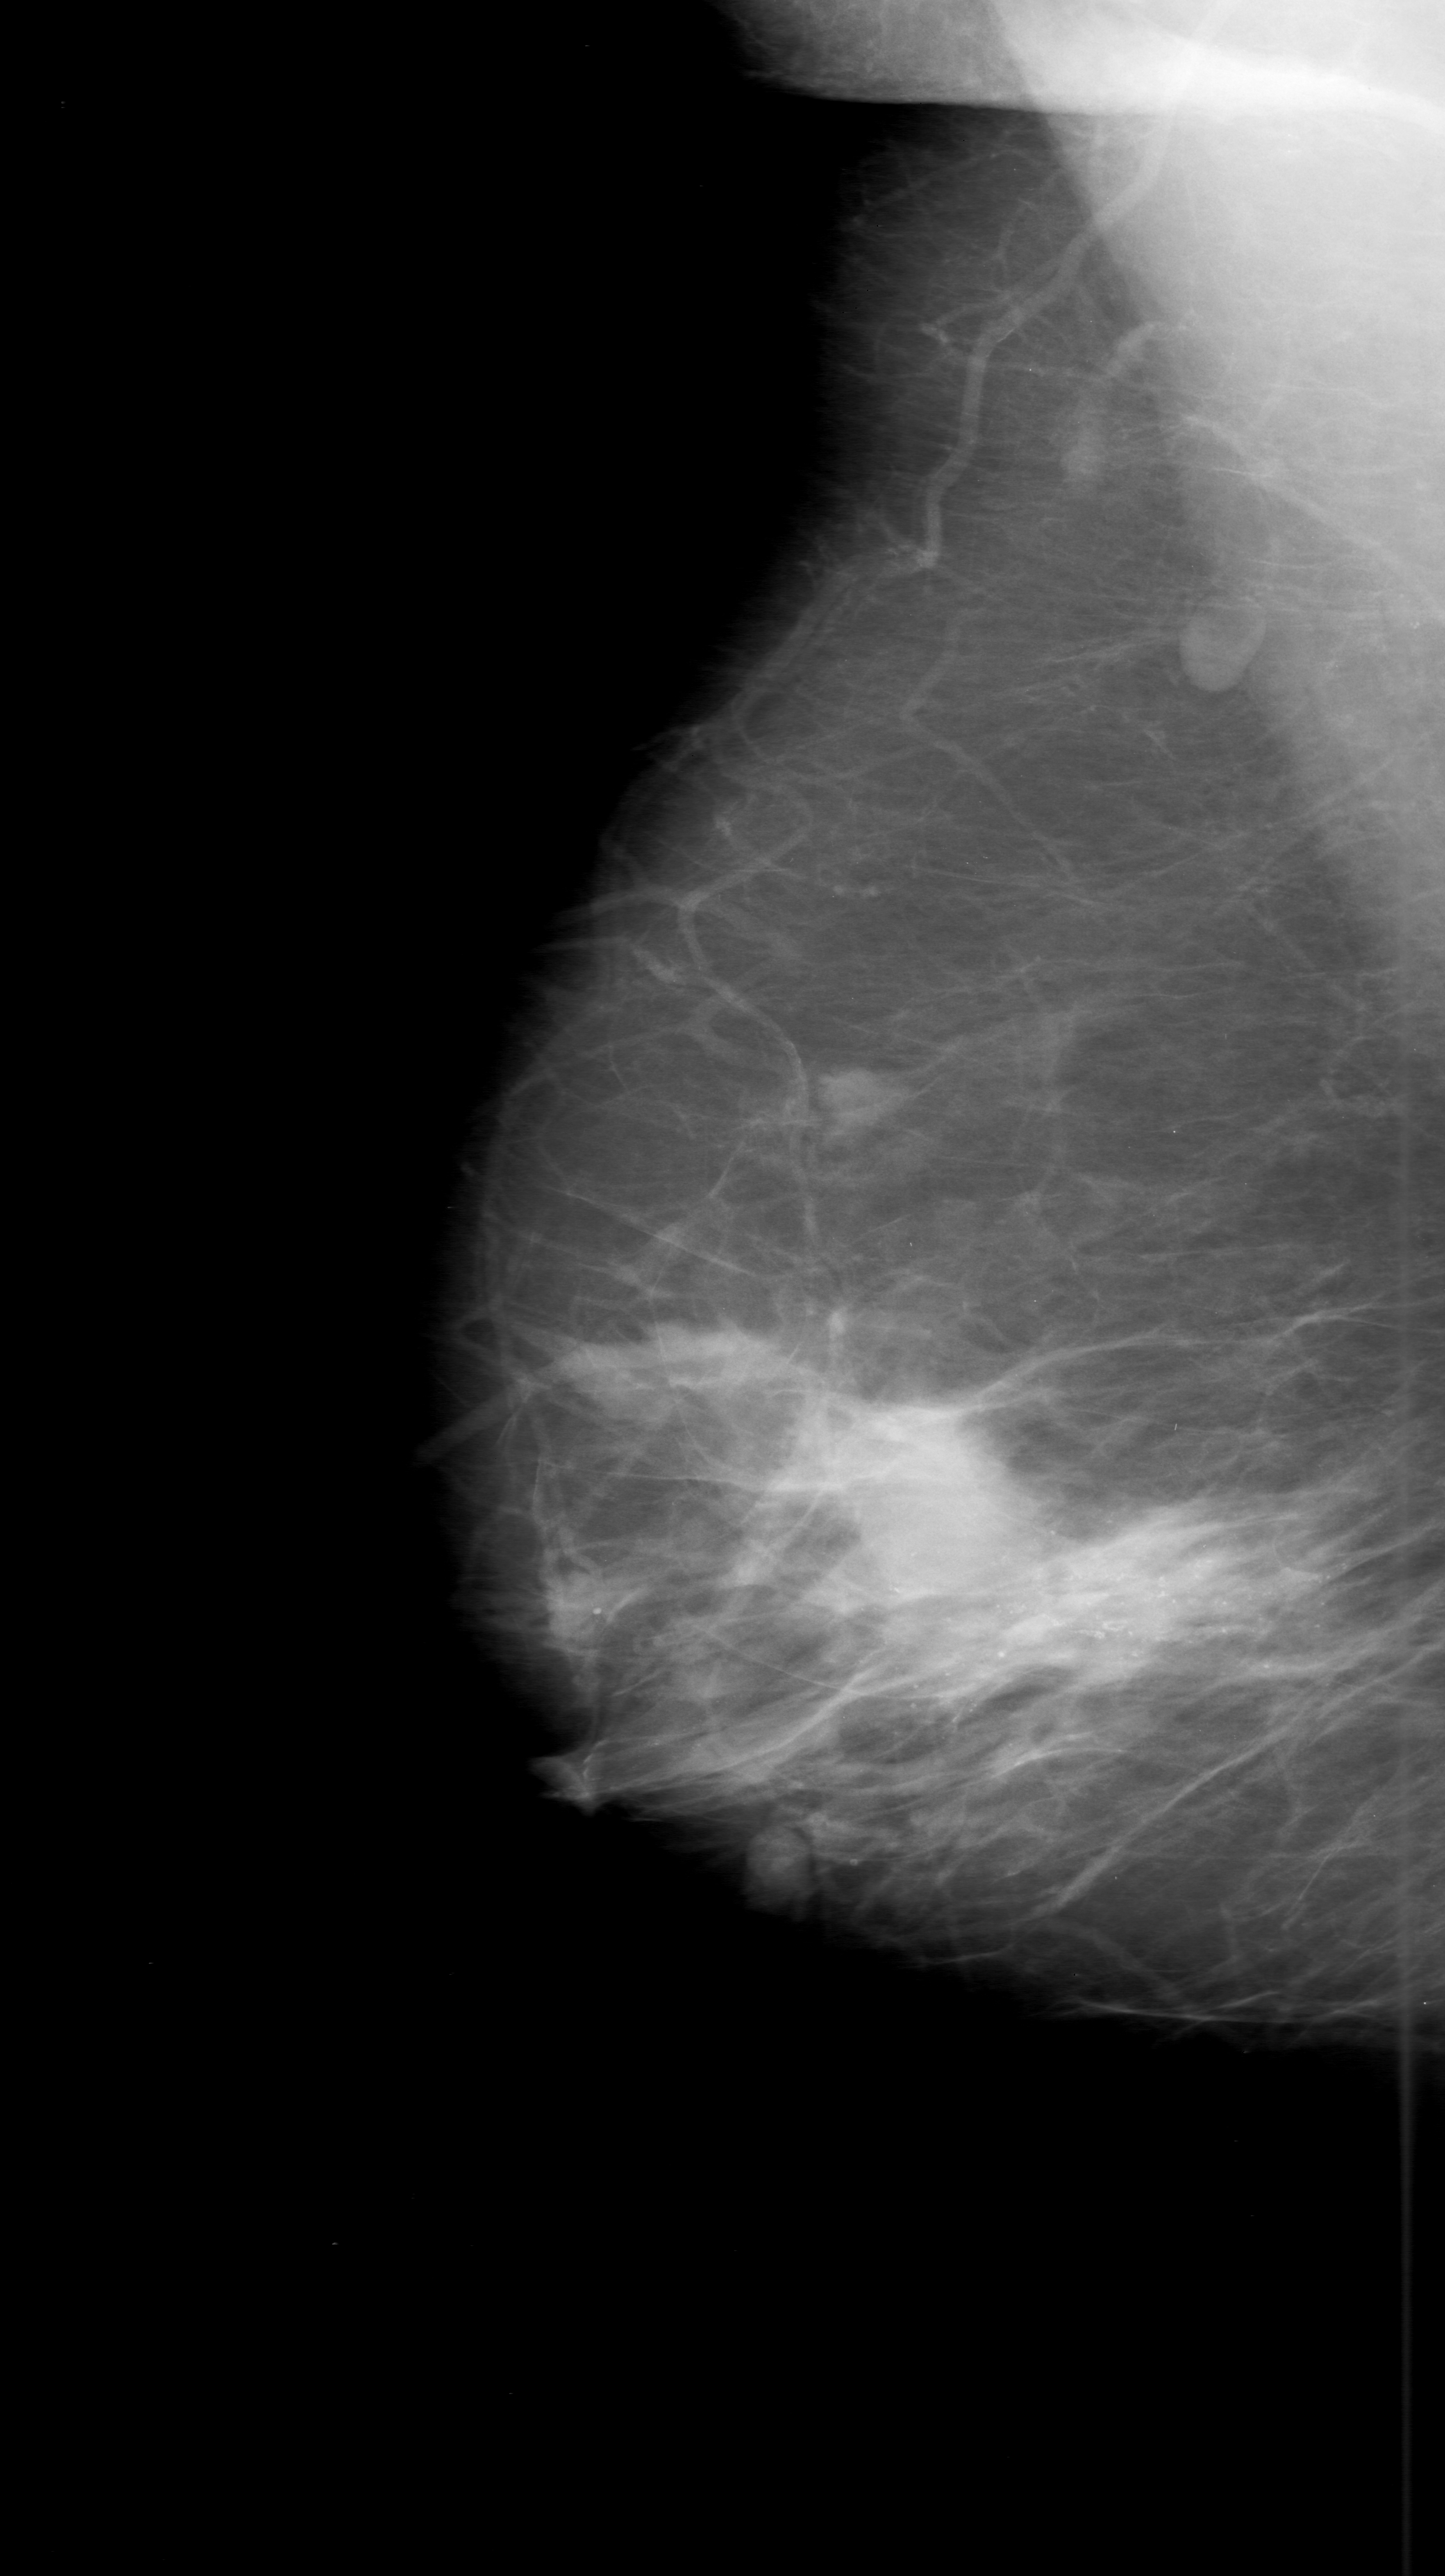
Scanned film-screen mammogram; right breast; MLO view; BI-RADS breast density category 2 (scale 1–4); 1445 × 2576 image matrix.
Marked abnormalities (boxes around the expert regions of interest):
- calcifications, morphology amorphous / pleomorphic, distribution segmental; BI-RADS assessment category 5; pathology (as recorded): malignant: bounding box (x1, y1, x2, y2) in pixels: (718, 1401, 1389, 1835)